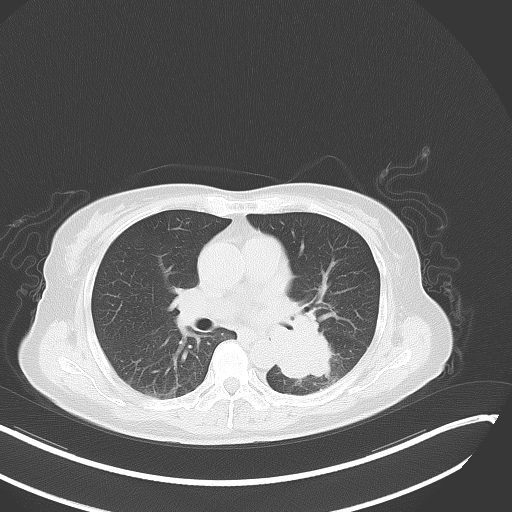
Chest CT, one axial slice. Position 21 of 48 along the scan axis. Reconstruction kernel B70f. Lung window (W 1500 / L -600 HU). 5 mm slice thickness. 512 × 512 image matrix, field of view 400 × 400 mm. Patient: female, 64 years. From the clinical record (not read from this slice): clinical TNM (as recorded): T3 N1 M1.
Annotated regions visible in this slice (bounding box drawn by a radiologist):
- lung tumour (recorded histology: small cell carcinoma): bounding box (x1, y1, x2, y2) in pixels: (266, 309, 336, 382)